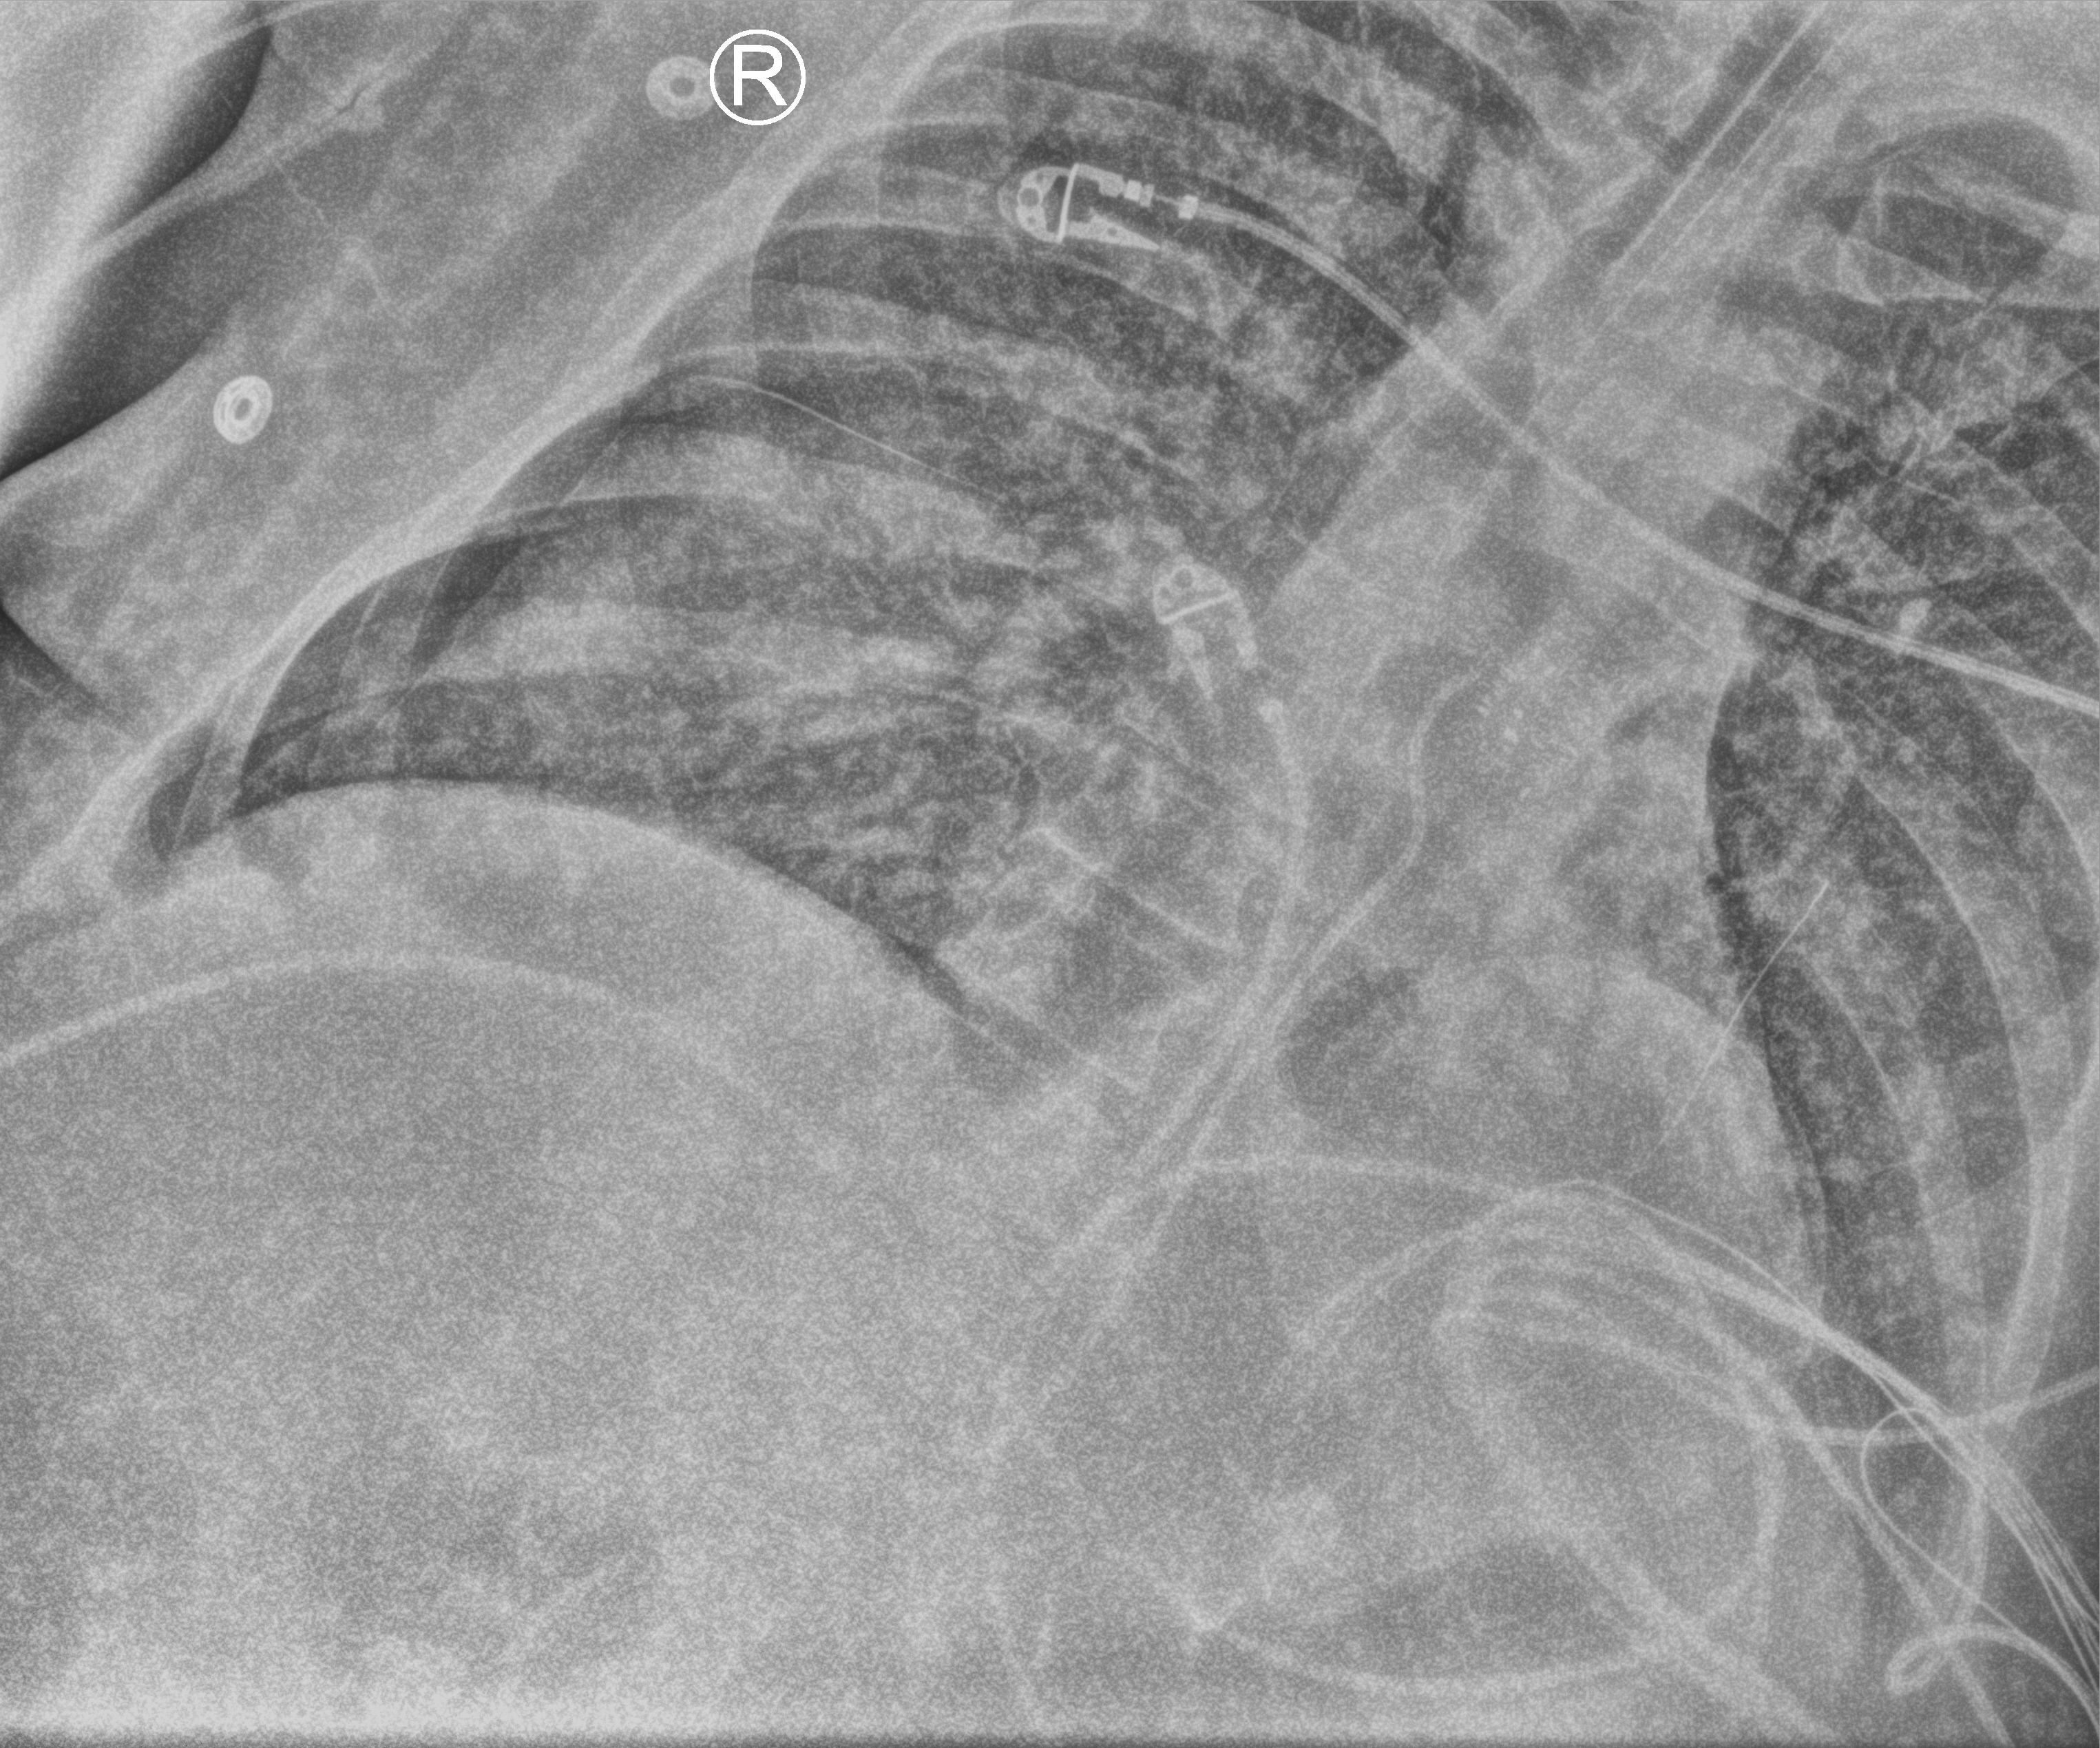
Chest X-ray (portable), anteroposterior (AP) projection. Patient hospitalised with COVID-19, aged 18–59 years.
Hospital-stay facts (about this admission, not read from this image; timing relative to this image not recorded): length of hospital stay: 26 days.